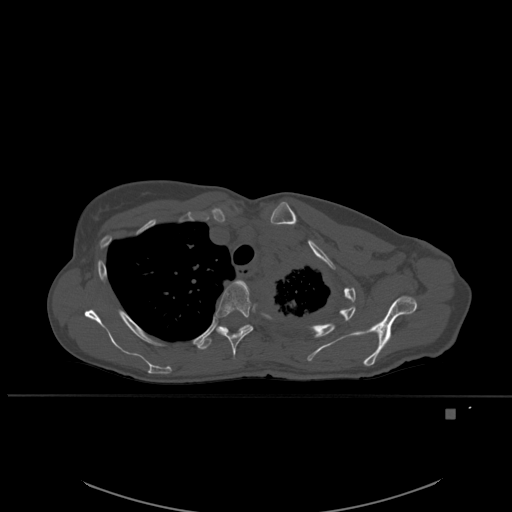
CT including the spine, one axial slice. Slice 410 of 537 in the series (ordered by position). Bone window (W 1800 / L 400 HU). 512 × 512 image matrix, field of view 440 × 440 mm. Female patient, age 45 years. From the clinical record (not read from this slice): primary cancer: lung.
Annotated regions visible in this slice (semi-automatic segmentation, software-assisted and operator-edited):
- T3 vertebra: bounding box (x1, y1, x2, y2) in pixels: (237, 280, 249, 293)
- T4 vertebra: (216, 282, 253, 360)
- T5 vertebra: (196, 324, 251, 350)